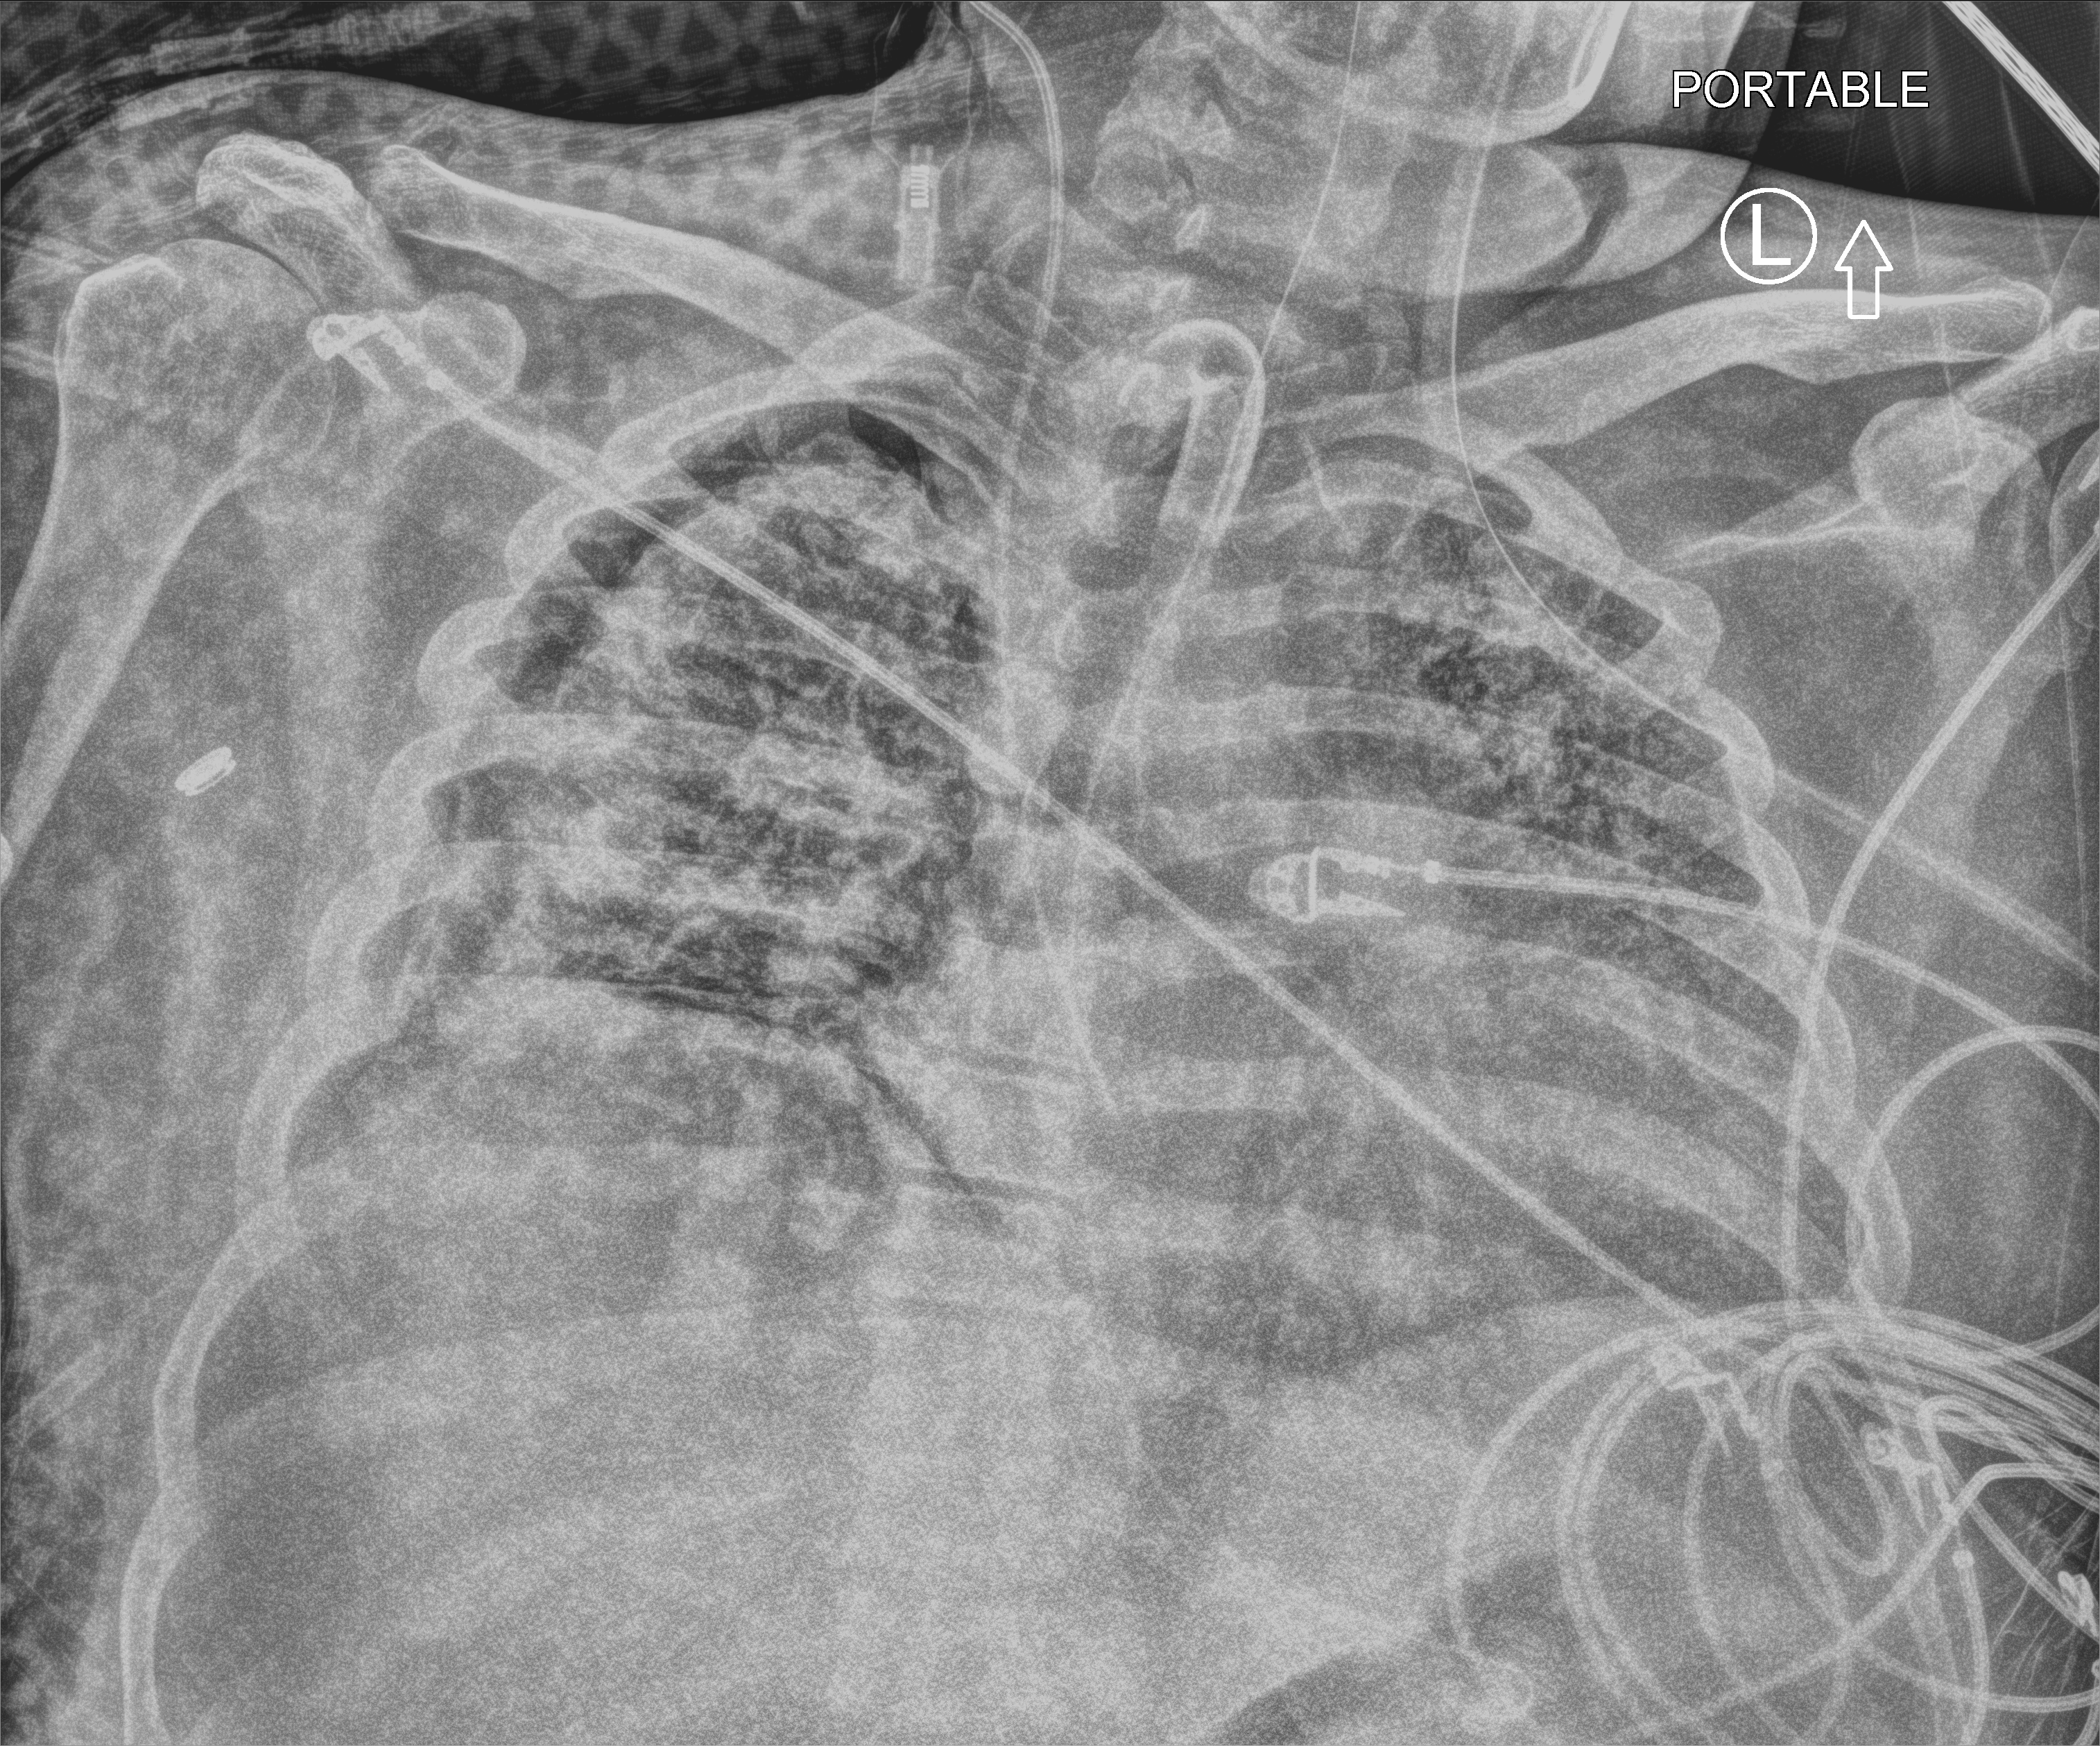
Chest X-ray (portable), anteroposterior (AP) projection. Male patient hospitalised with COVID-19, age 18–59 years.
From the hospital-stay record, not from the radiograph (when in the stay this image was taken is not recorded): mechanically ventilated during this hospital stay: yes.